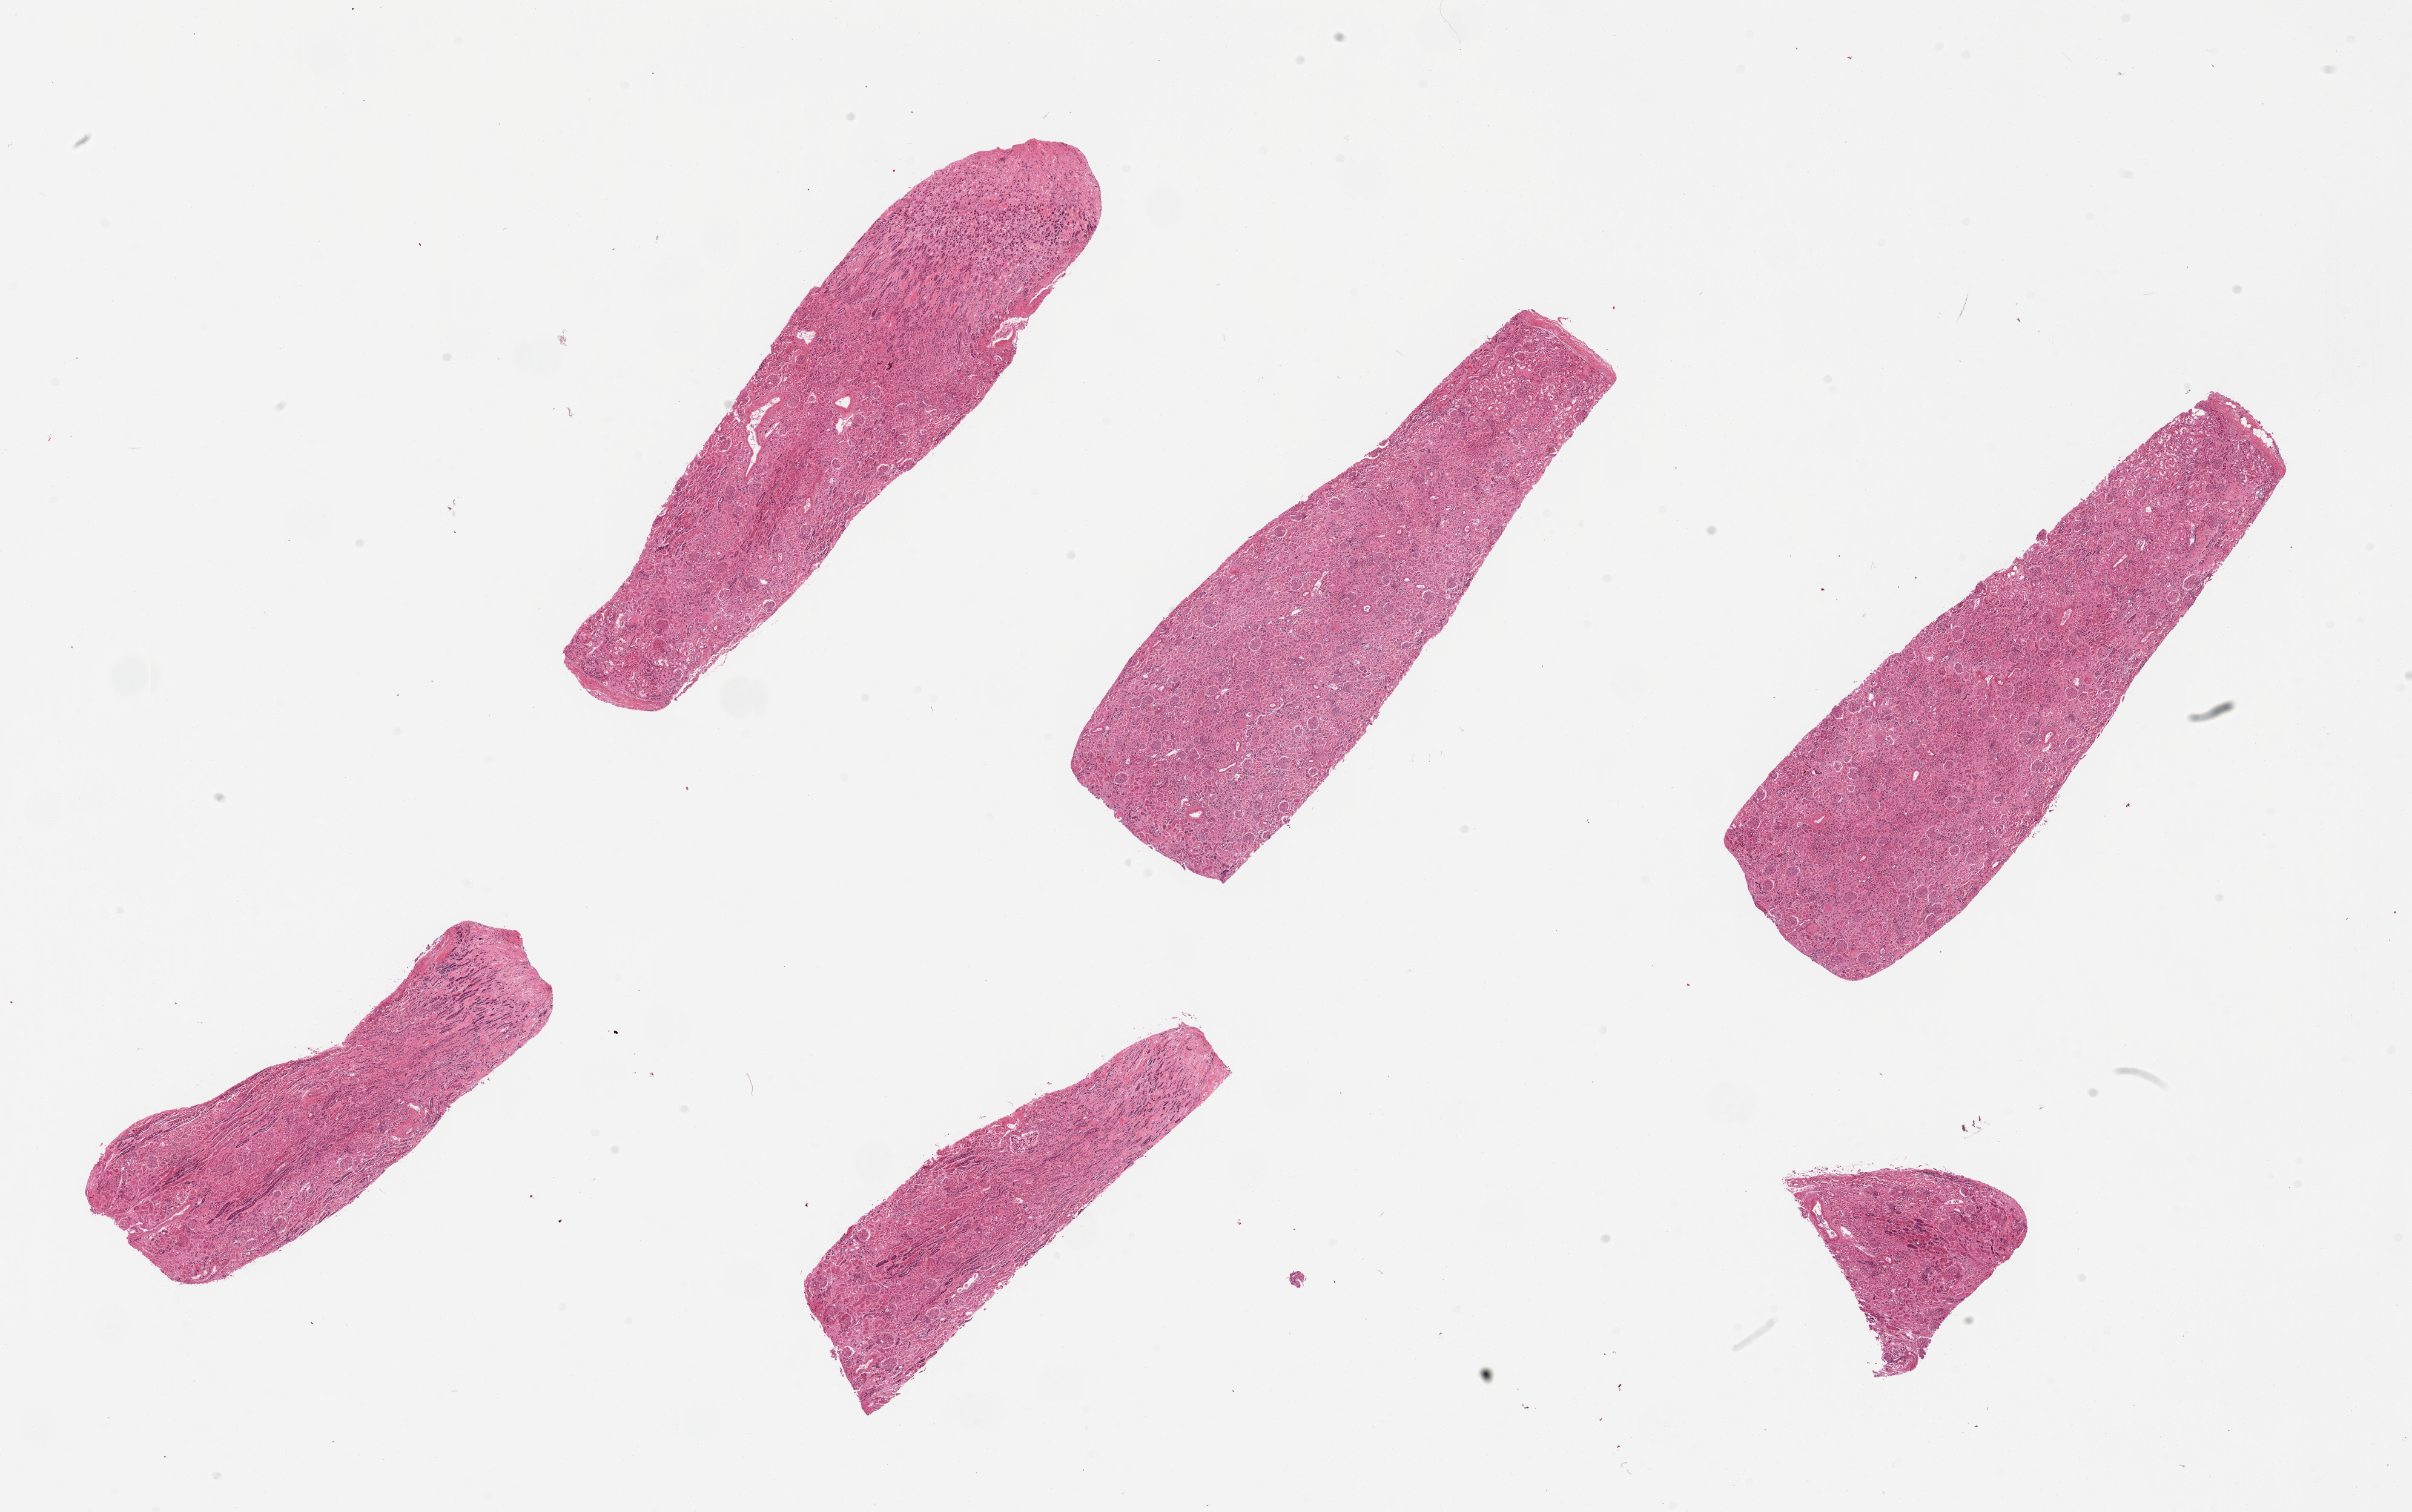
Digitized hematoxylin and eosin (H&E)-stained section, low-resolution overview of the scanned area, about 31.5 x 19.7 mm. PAXgene-fixed paraffin-embedded (PFPE) section. Target tissue: renal cortex. Tissue donor sample.
Review note (as recorded): 6 pieces glomeruli present.